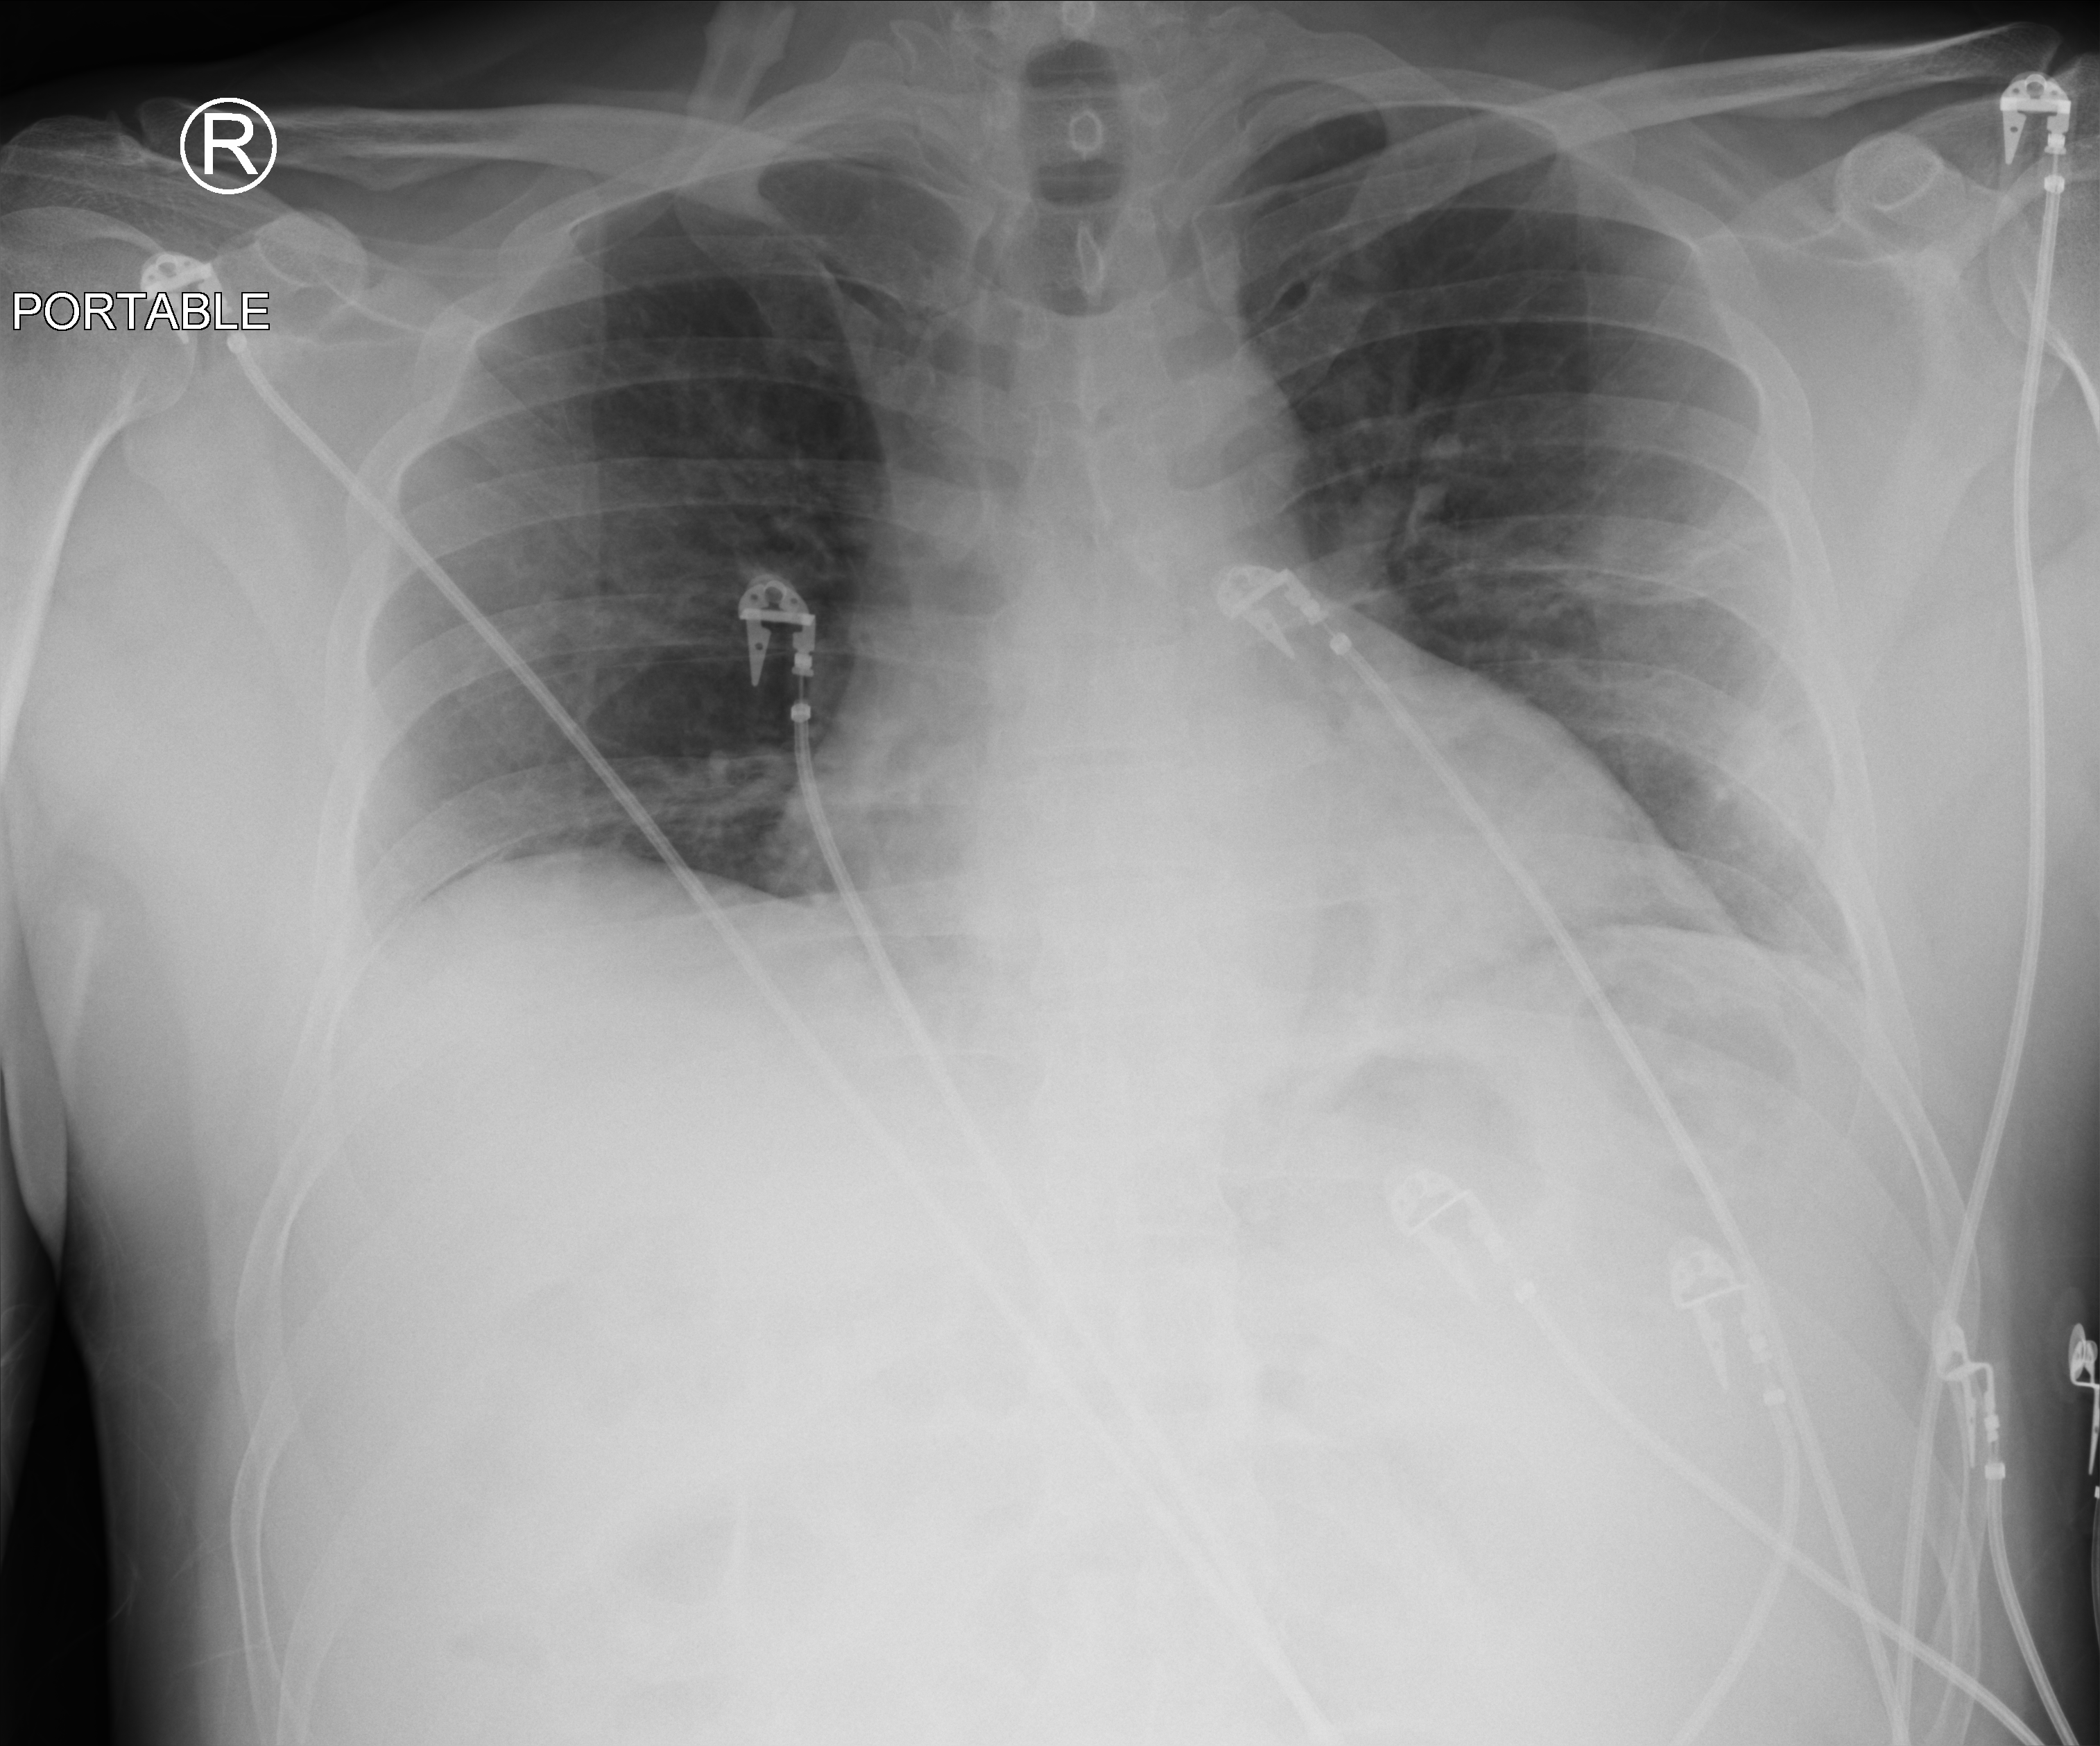
Chest X-ray (portable); anteroposterior (AP) projection. Patient hospitalised with COVID-19; male, aged 18–59 years.
From the hospital-stay record, not from the radiograph (when in the stay this image was taken is not recorded):
- length of hospital stay: 8 days